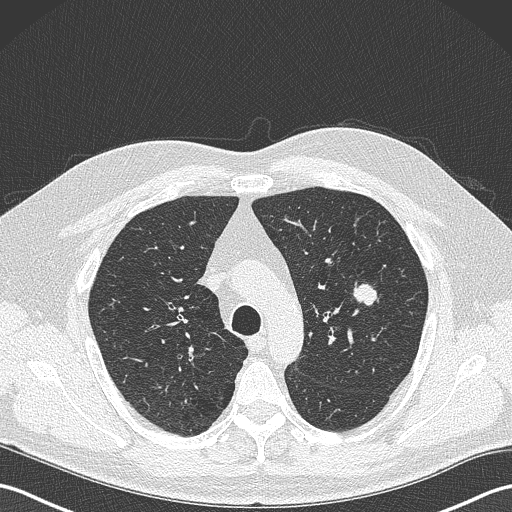
Low-dose screening chest CT, one axial slice. Position 248 of 343 along the scan axis. Reconstruction kernel B50f. Lung window (W 1500 / L -600 HU). 1 mm slice thickness. 512 × 512 image matrix, field of view 350 × 350 mm.
Annotated regions visible in this slice (expert manual segmentation):
- lesion 1 (tumor, upper lobe of left lung): bounding box [x1, y1, x2, y2] px = [354, 282, 381, 306]